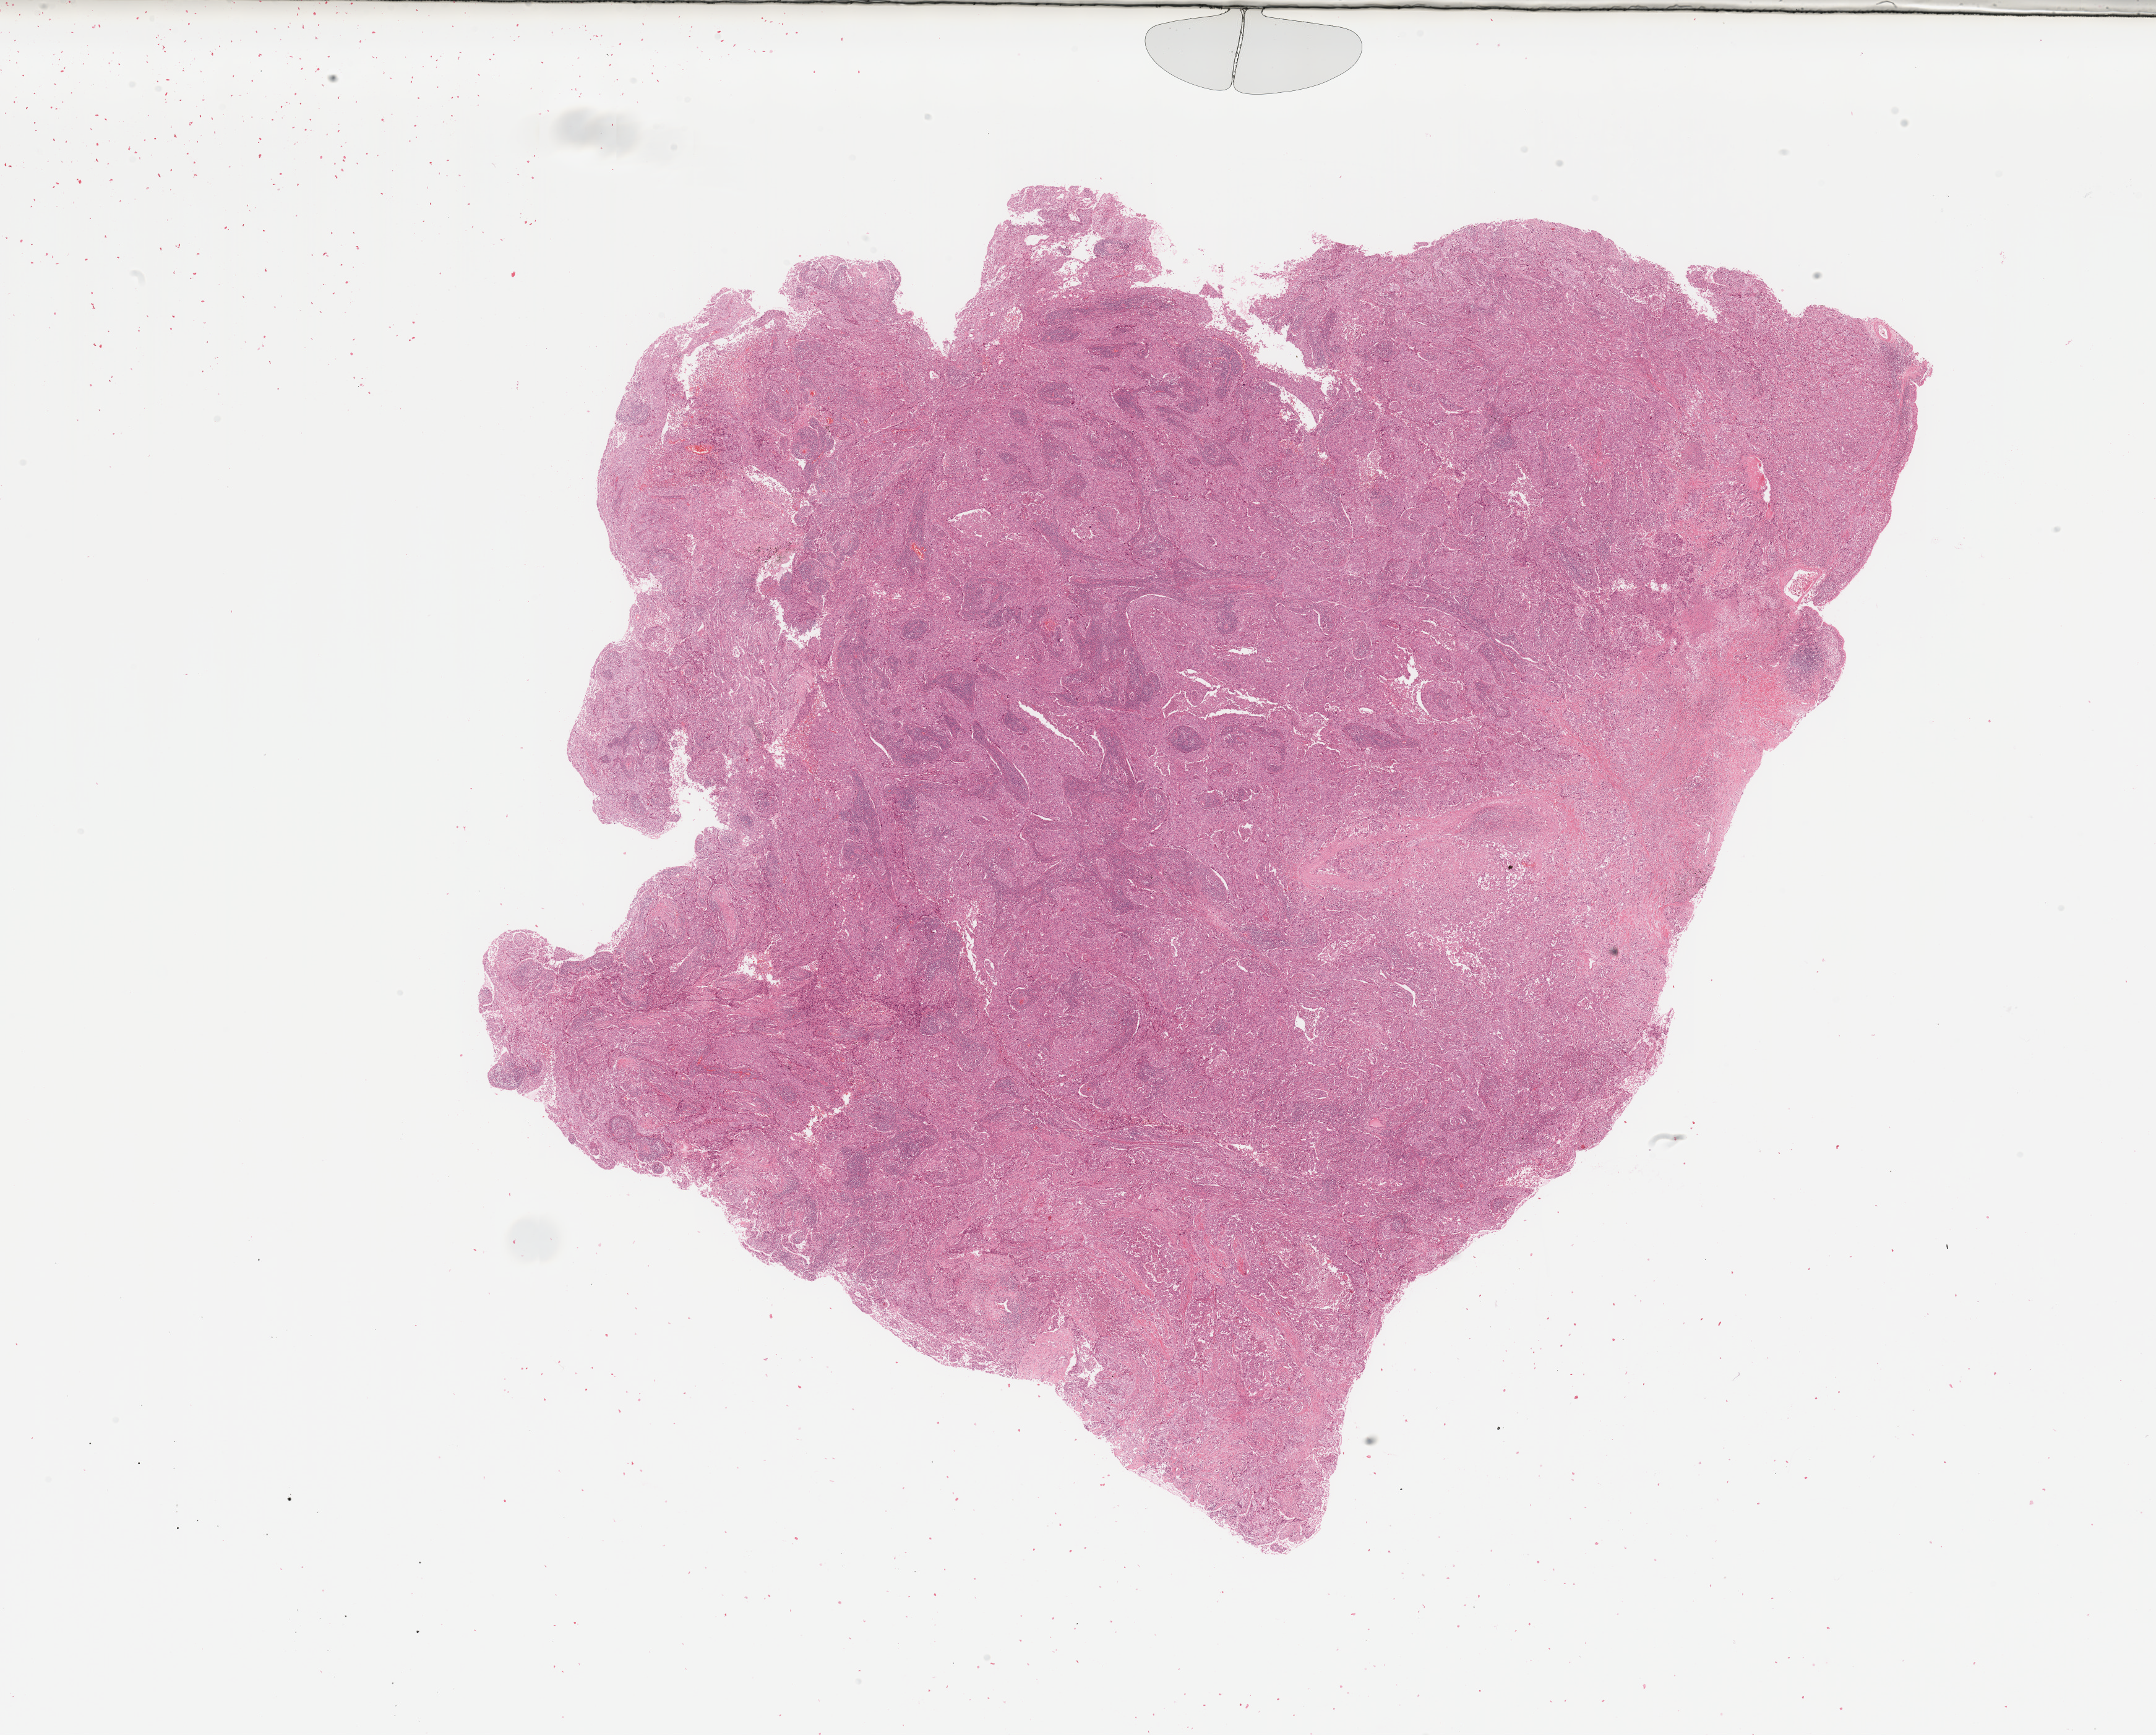
Hematoxylin and eosin (H&E) stained whole-slide image — whole scanned area (about 27.6 x 22.2 mm, slide scanned at 20x) shown as a low-resolution overview; tumour tissue sample, lung. Patient: male, age 60 years. Histologic grade: G3 (poorly differentiated).
AJCC pathologic stage: IIB. Diagnosis: Adenocarcinoma, NOS.